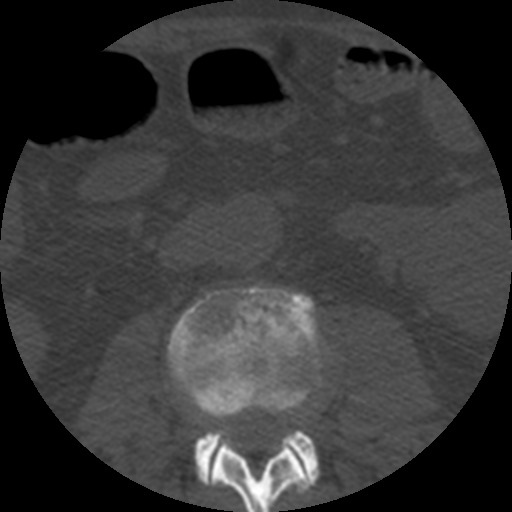
CT including the spine, one axial slice; slice 136 of 508 in the series (ordered by position); reconstruction kernel STANDARD; bone window (W 1800 / L 400 HU); 1.25 mm slice thickness; 512 × 512 image matrix, field of view 160 × 160 mm. Patient age 57 years. From the clinical record (not read from this slice): primary cancer: prostate.
Structures marked on this image (semi-automatic segmentation, software-assisted and operator-edited):
- L2 vertebra: bounding box <203,426,313,512> (left, top, right, bottom; pixels)
- L3 vertebra: <168,286,323,482>